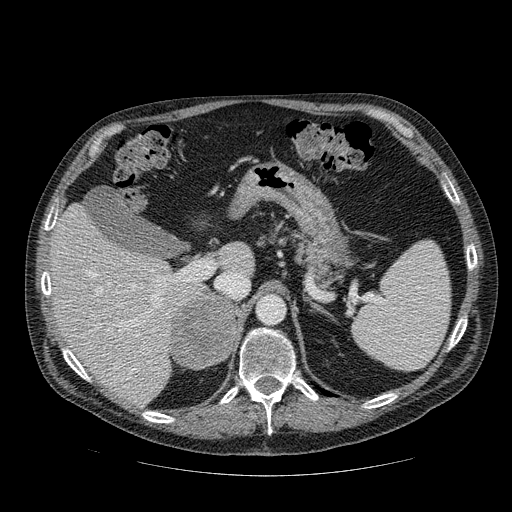
Contrast-enhanced abdominal CT, one axial slice. Slice 63 of 111 in the series (ordered by position). Reconstruction kernel STANDARD. 120 kVp. Intravenous contrast given. Soft-tissue window (W 400 / L 40 HU). 512 × 512 image matrix. Male patient, age 56 years. Case-level facts recorded for this patient, not image findings: diagnosis: adrenocortical carcinoma; tumour side: right adrenal; tumour size at pathology: 9 cm.
Outlined on this slice (semi-automatic segmentation, software-assisted and operator-edited):
- mass: bounding box (x1, y1, x2, y2) in pixels: (171, 297, 236, 368)